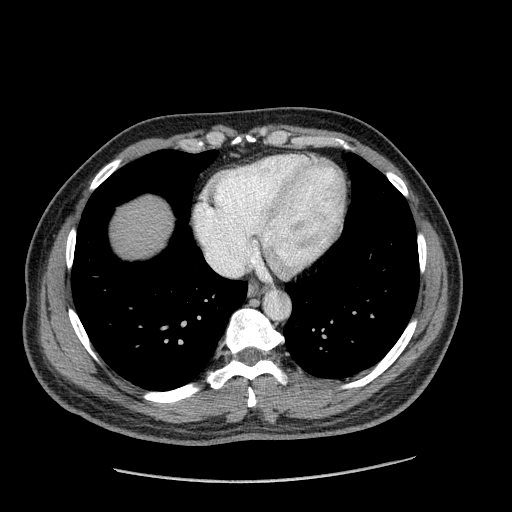
Contrast-enhanced abdominal CT (liver protocol), one axial slice; position 173 of 182 along the scan axis; soft-tissue window (W 400 / L 40 HU); 512 × 512 image matrix. From the clinical record (not read from this slice): diagnosis: hepatocellular carcinoma (patient treated with transarterial chemoembolisation; whether this scan precedes or follows treatment is not stated here); TNM stage (as recorded): Stage-I; Child-Pugh class: A; tumour differentiation: well differentiated; tumour nodularity: uninodular.
Outlined on this slice (semi-automatically segmented with operator editing):
- abdominal aorta: bounding box (x1, y1, x2, y2) in pixels: (263, 291, 289, 319)
- liver parenchyma outside the tumour (the mass and vessels are separate outlines, so this box may not span the whole liver): (114, 196, 172, 256)